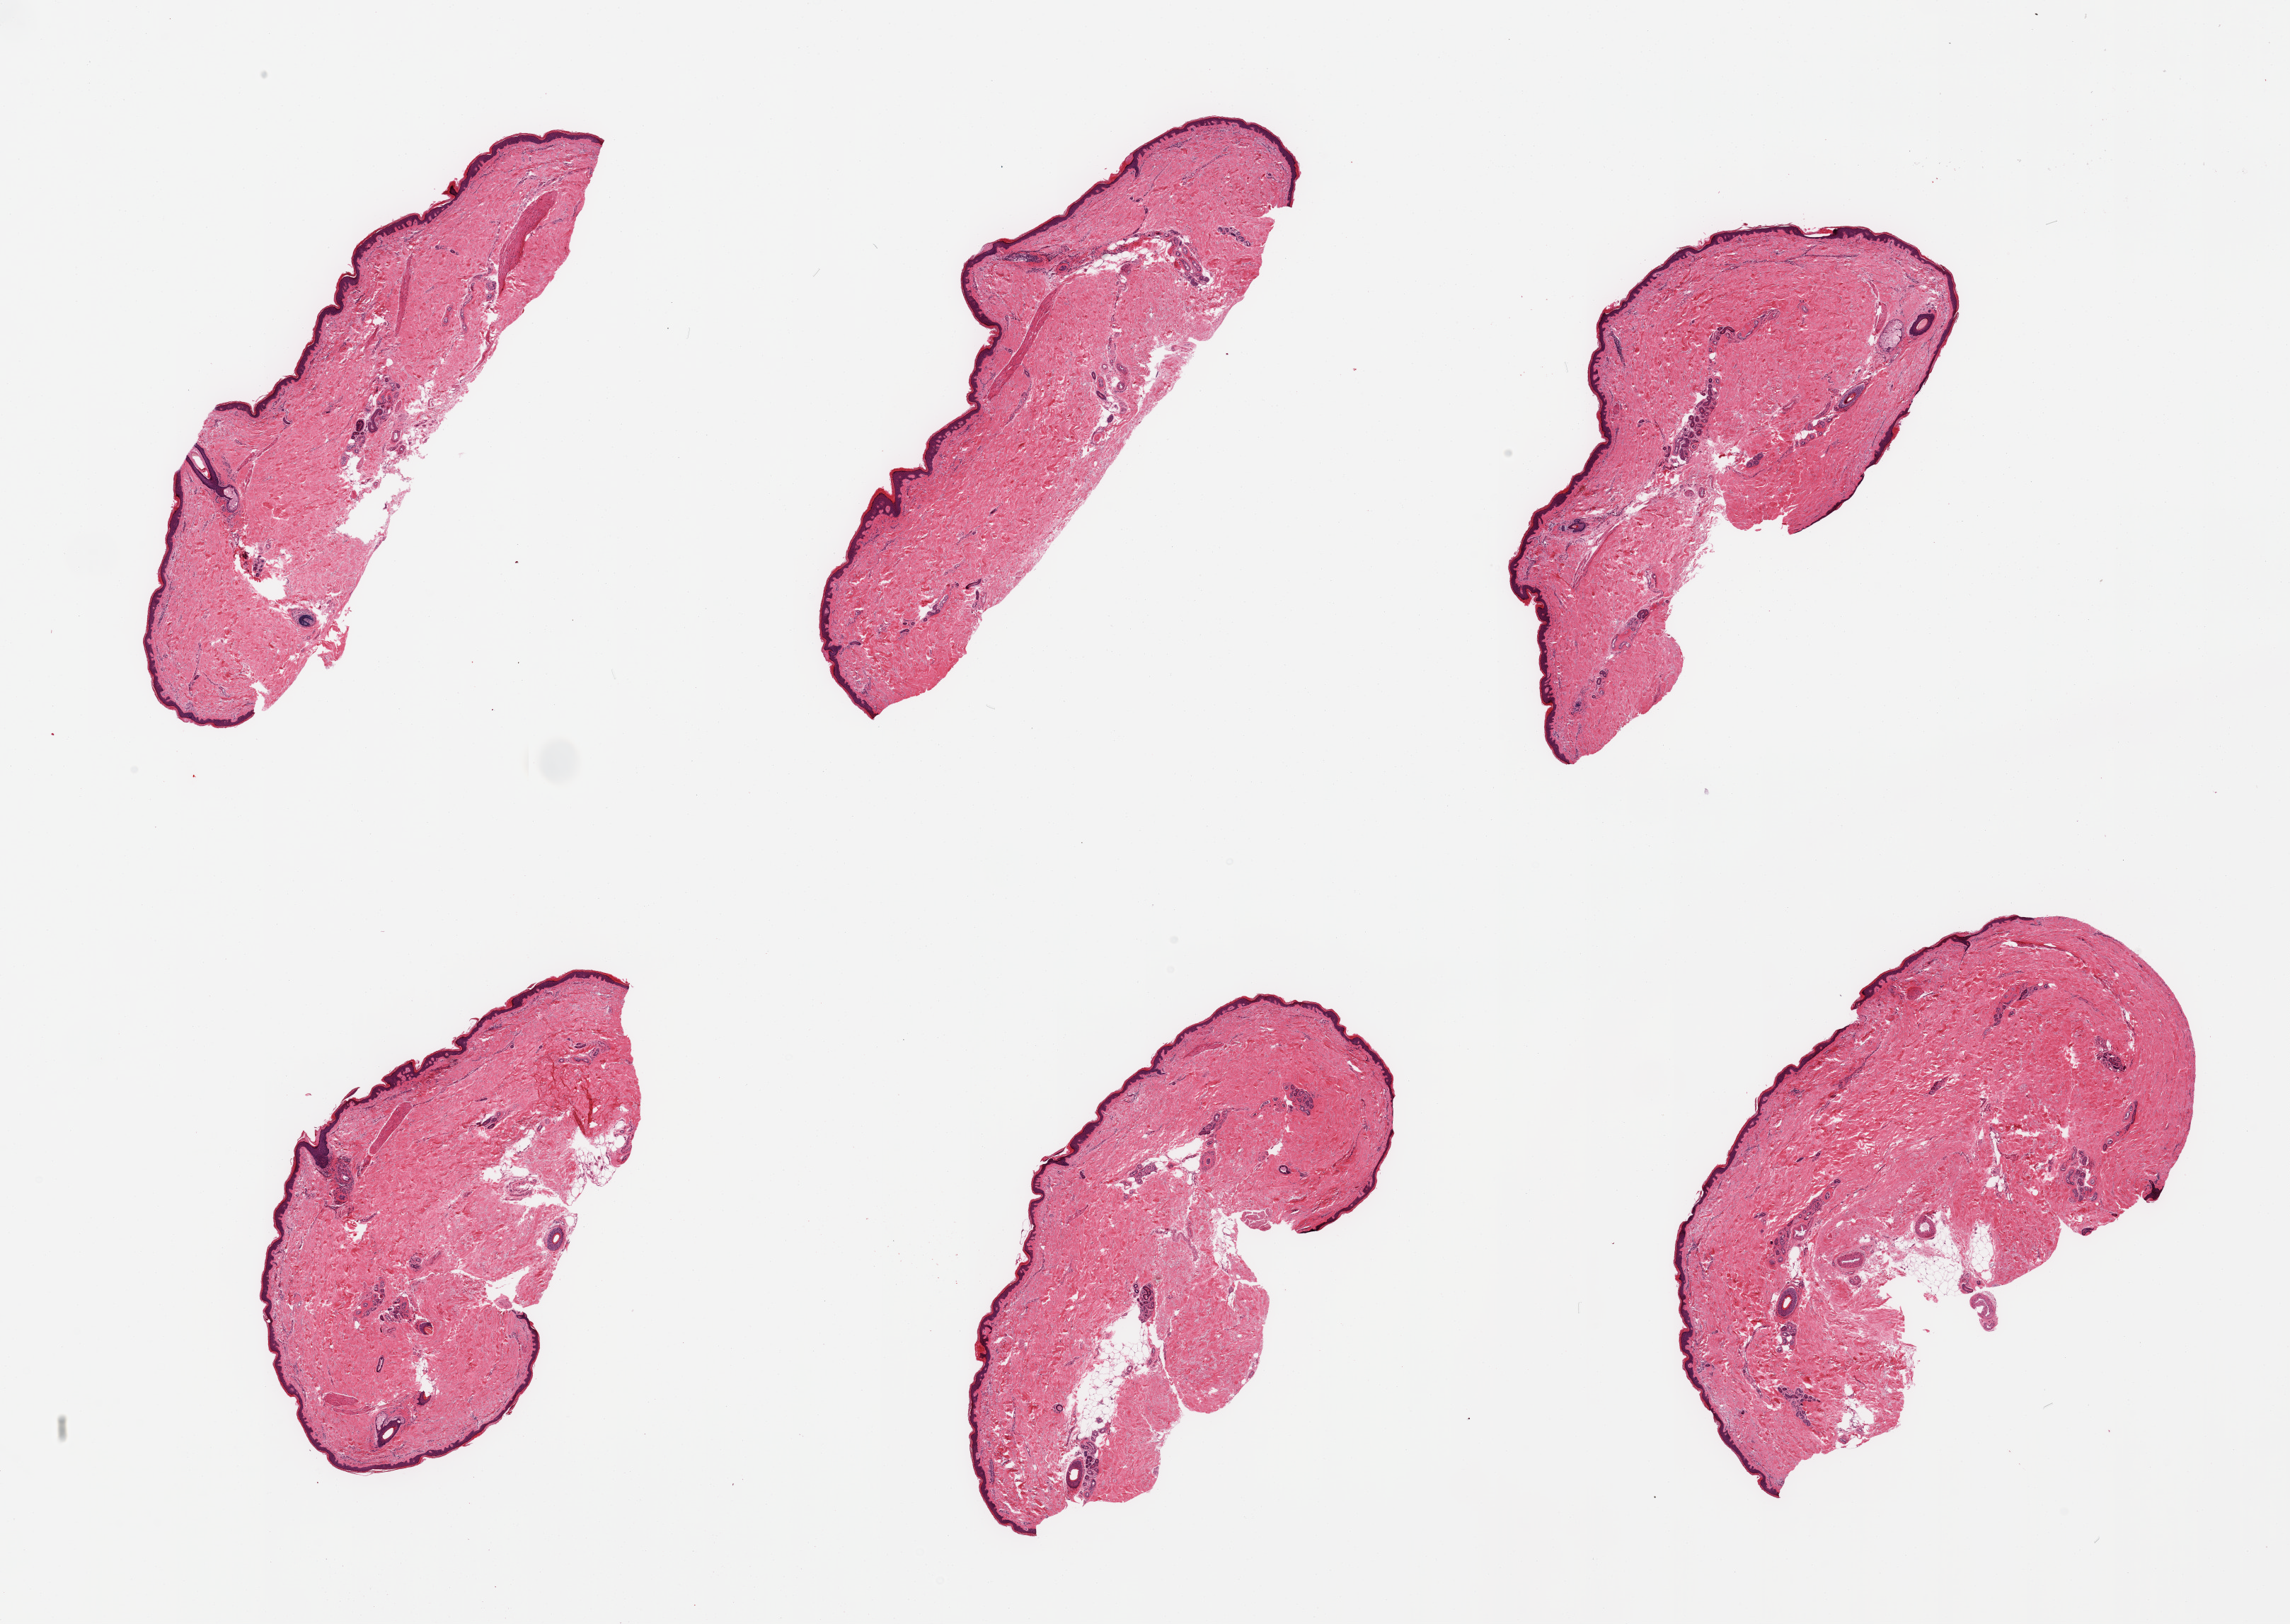
H&E whole-slide image, brightfield — shown as a low-resolution overview of the whole scanned area (about 25.6 x 18.2 mm), PAXgene-fixed paraffin-embedded (PFPE) section, target tissue: skin of lower leg, tissue donor sample. Male donor.
Pathologist's review note for this sample: 6 pieces, minimal dermal fat; squamous epithelium is ~40-45 microns.